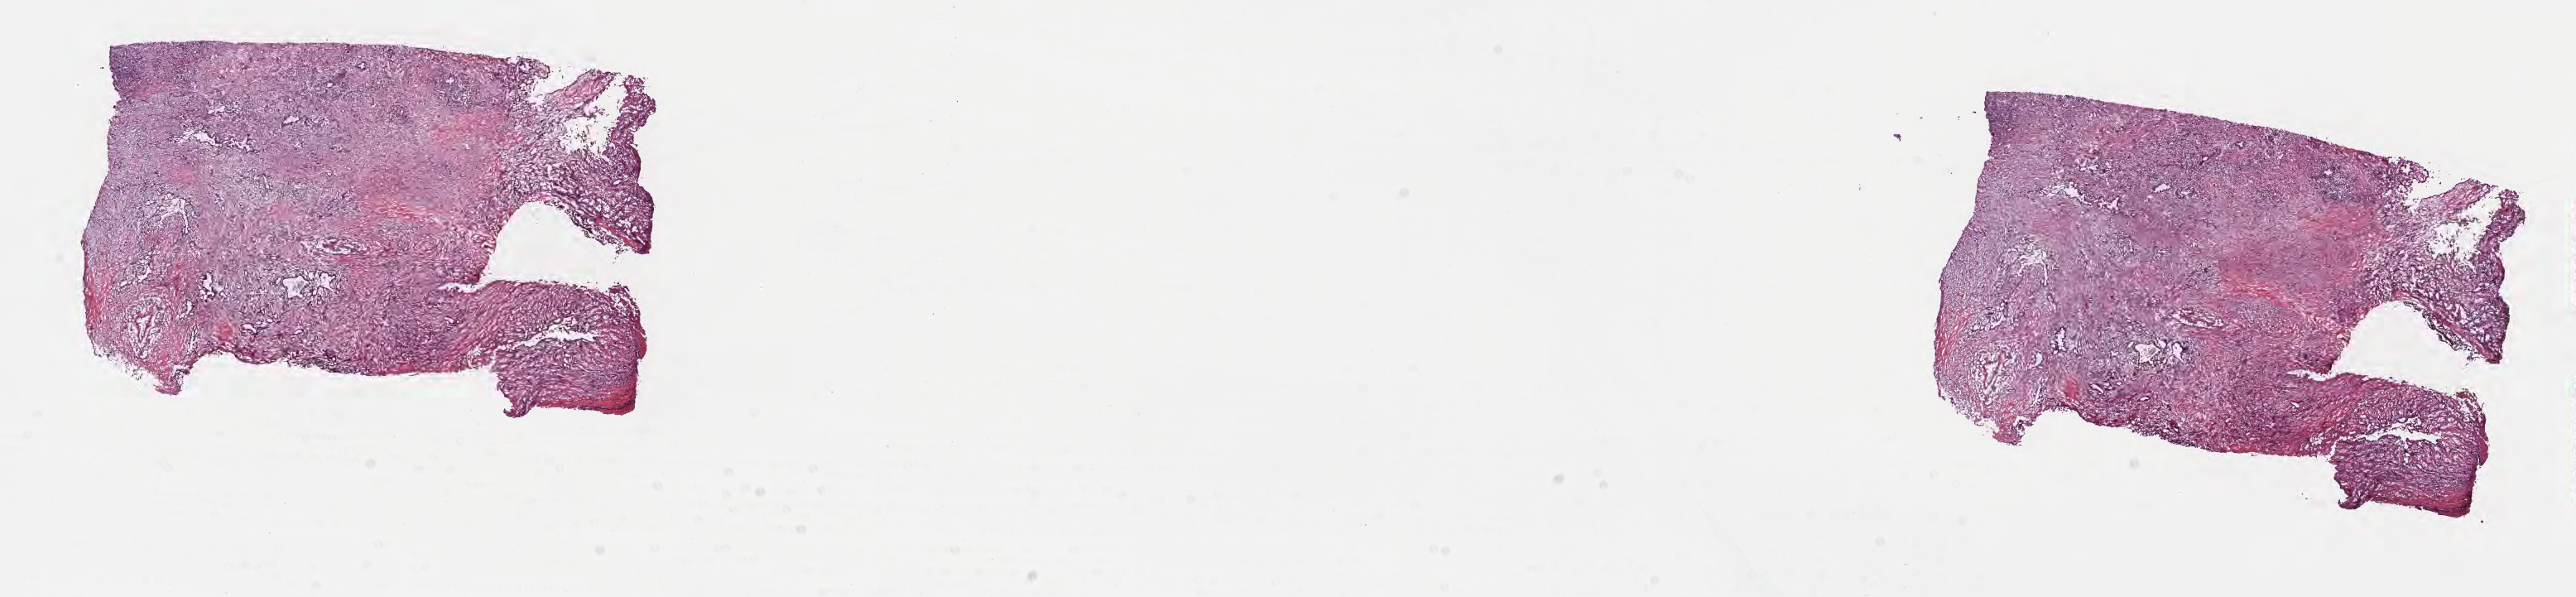
Whole-slide image, hematoxylin and eosin (H&E) stain — whole scanned area (about 25.2 x 5.8 mm) shown as a low-resolution overview; frozen section; primary tumor; anatomic site: tail of pancreas. Female, age 79 years at initial diagnosis.
Histologic diagnosis: Infiltrating duct carcinoma, NOS.